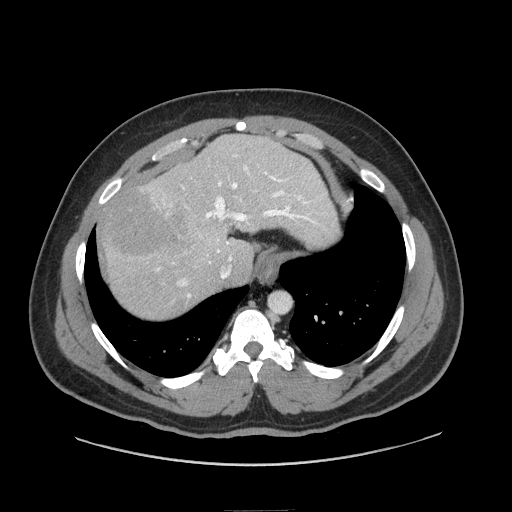
Contrast-enhanced abdominal CT (liver protocol), one axial slice; 140 kVp; soft-tissue window (W 400 / L 40 HU); 2.5 mm slice thickness; 512 × 512 image matrix, field of view 440 × 440 mm. Case-level facts recorded for this patient, not image findings: diagnosis: hepatocellular carcinoma (patient treated with transarterial chemoembolisation; whether this scan precedes or follows treatment is not stated here); TNM stage (as recorded): Stage-II; Child-Pugh class: A; tumour nodularity: uninodular.
Annotated regions visible in this slice (semi-automatically segmented with operator editing):
- liver parenchyma outside the tumour (the mass and vessels are separate outlines, so this box may not span the whole liver): bounding box (x1, y1, x2, y2) in pixels: (102, 134, 338, 318)
- mass: (98, 181, 194, 263)
- liver vessels: (157, 155, 309, 297)